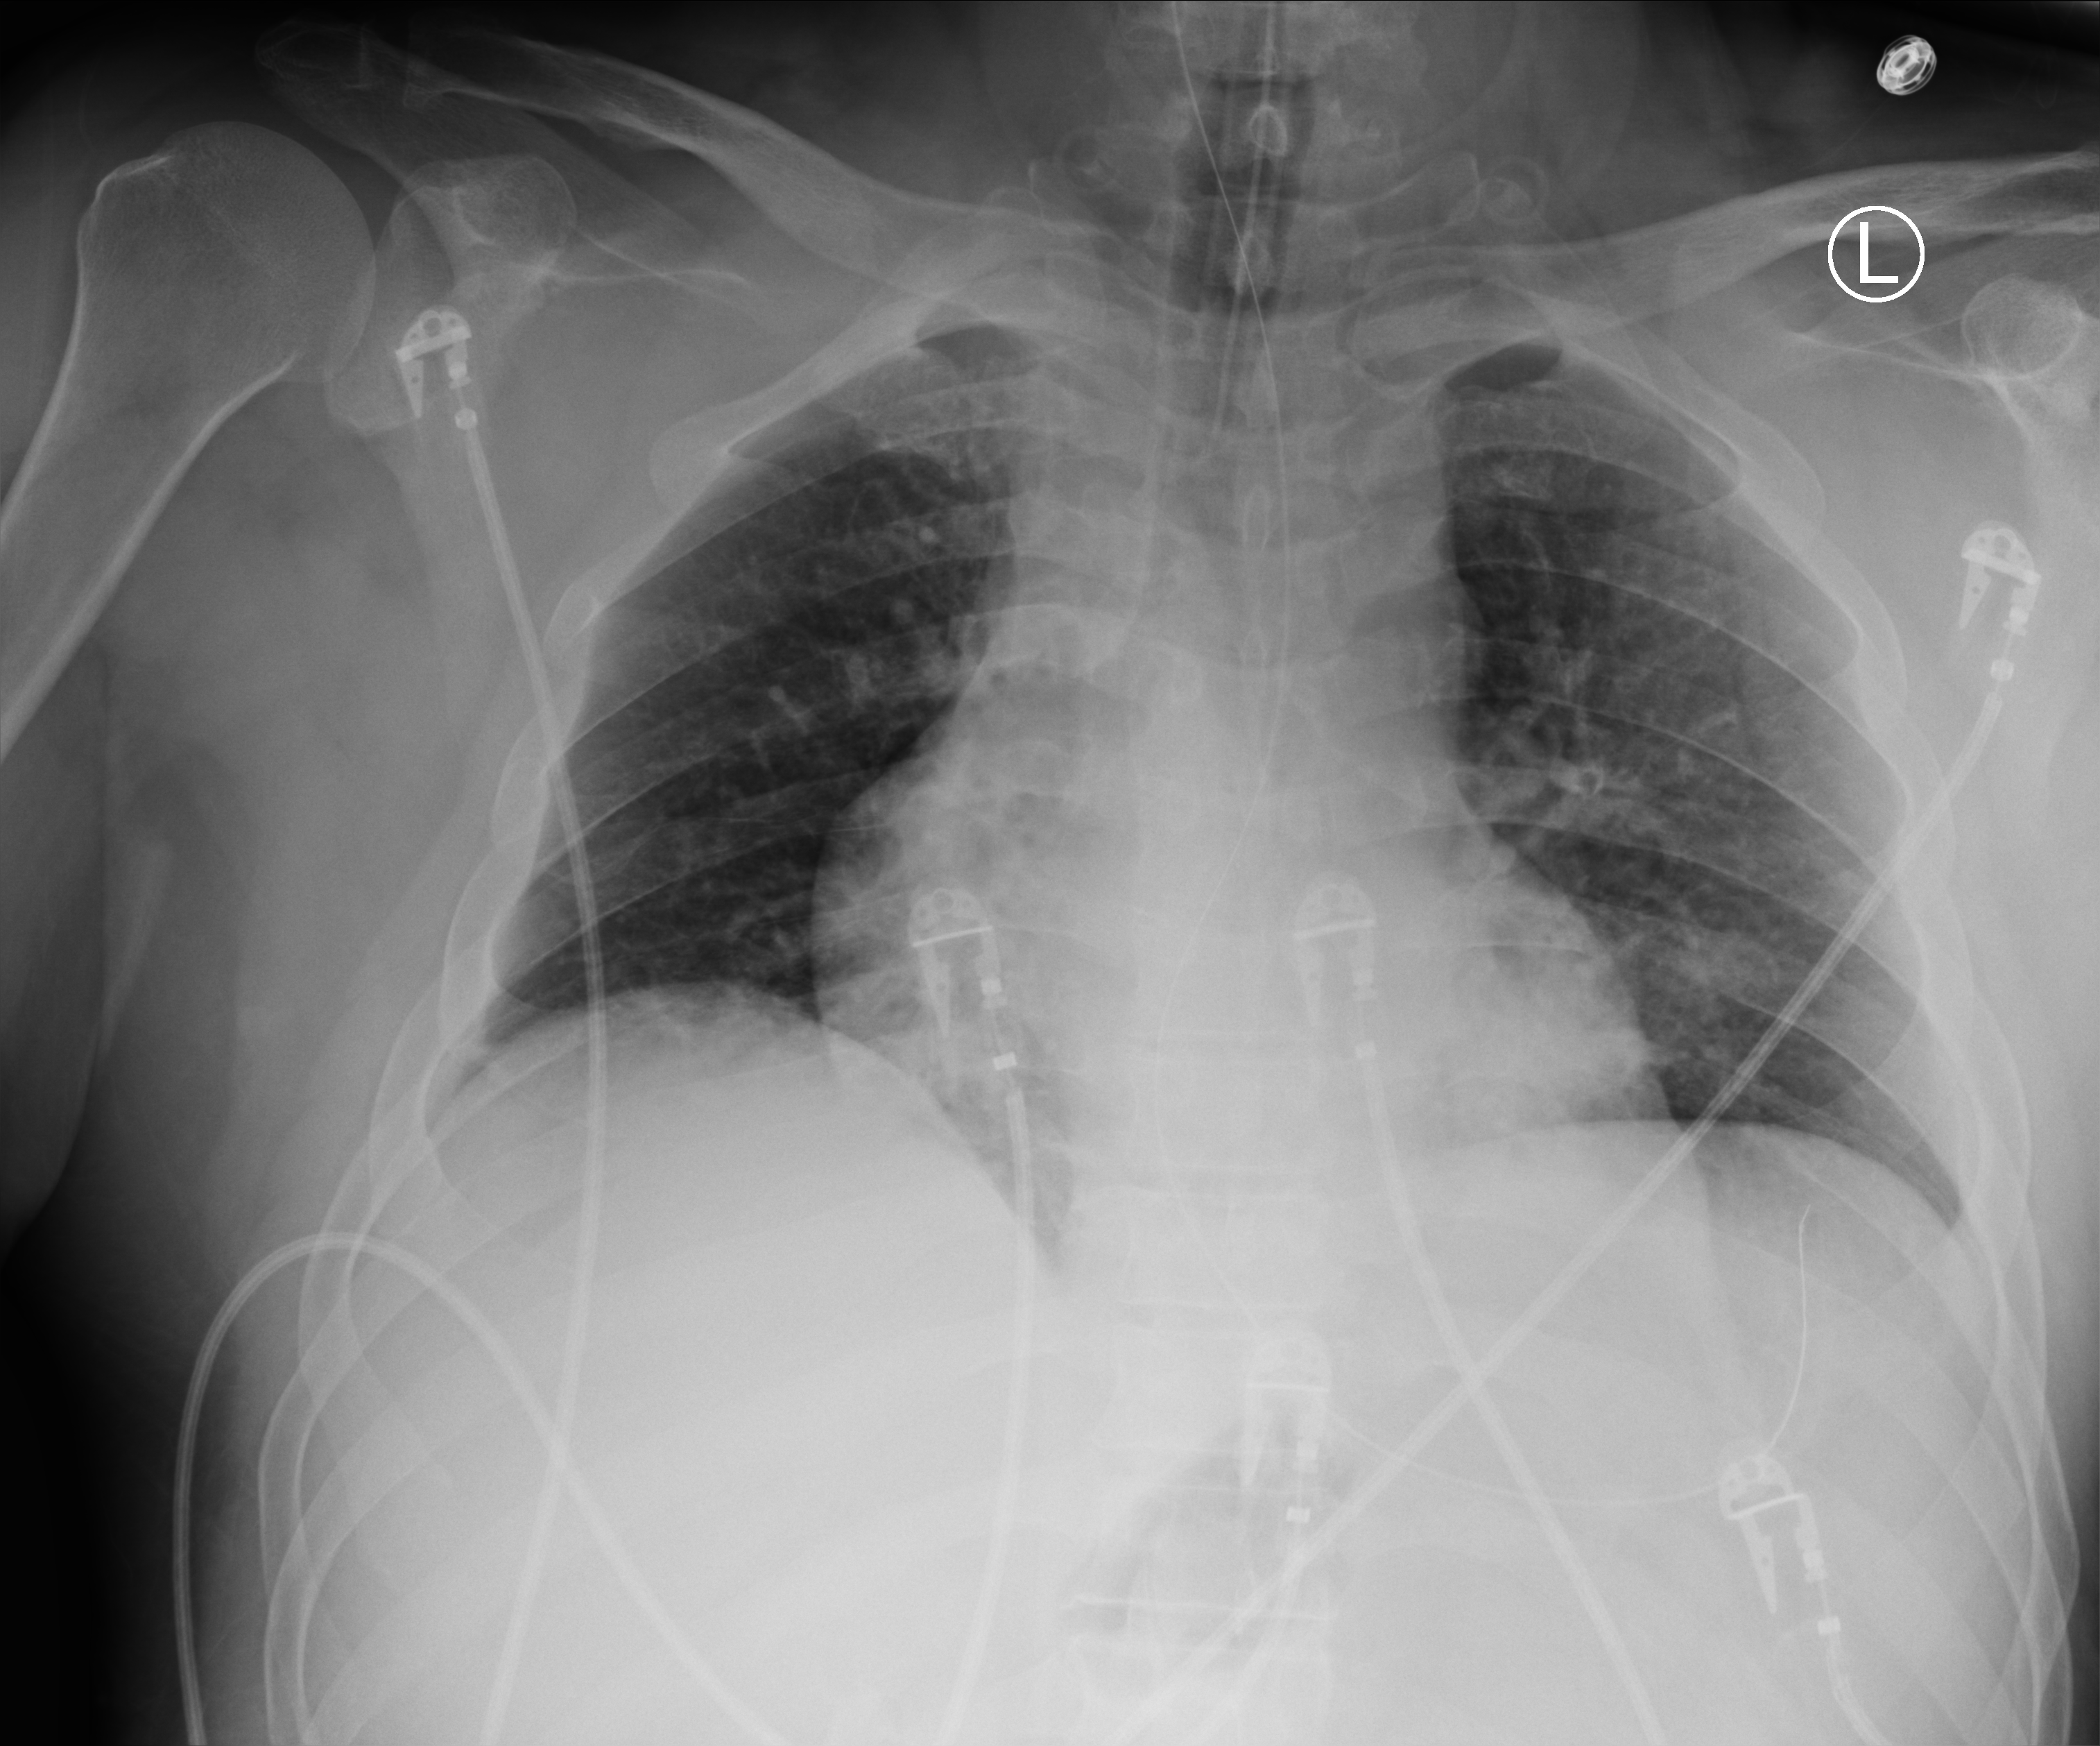
Portable chest radiograph, anteroposterior (AP) projection. Male patient hospitalised with COVID-19, age 18–59 years.
From the hospital-stay record, not from the radiograph (when in the stay this image was taken is not recorded): mechanically ventilated during this hospital stay: yes; admitted to intensive care during this hospital stay: yes.